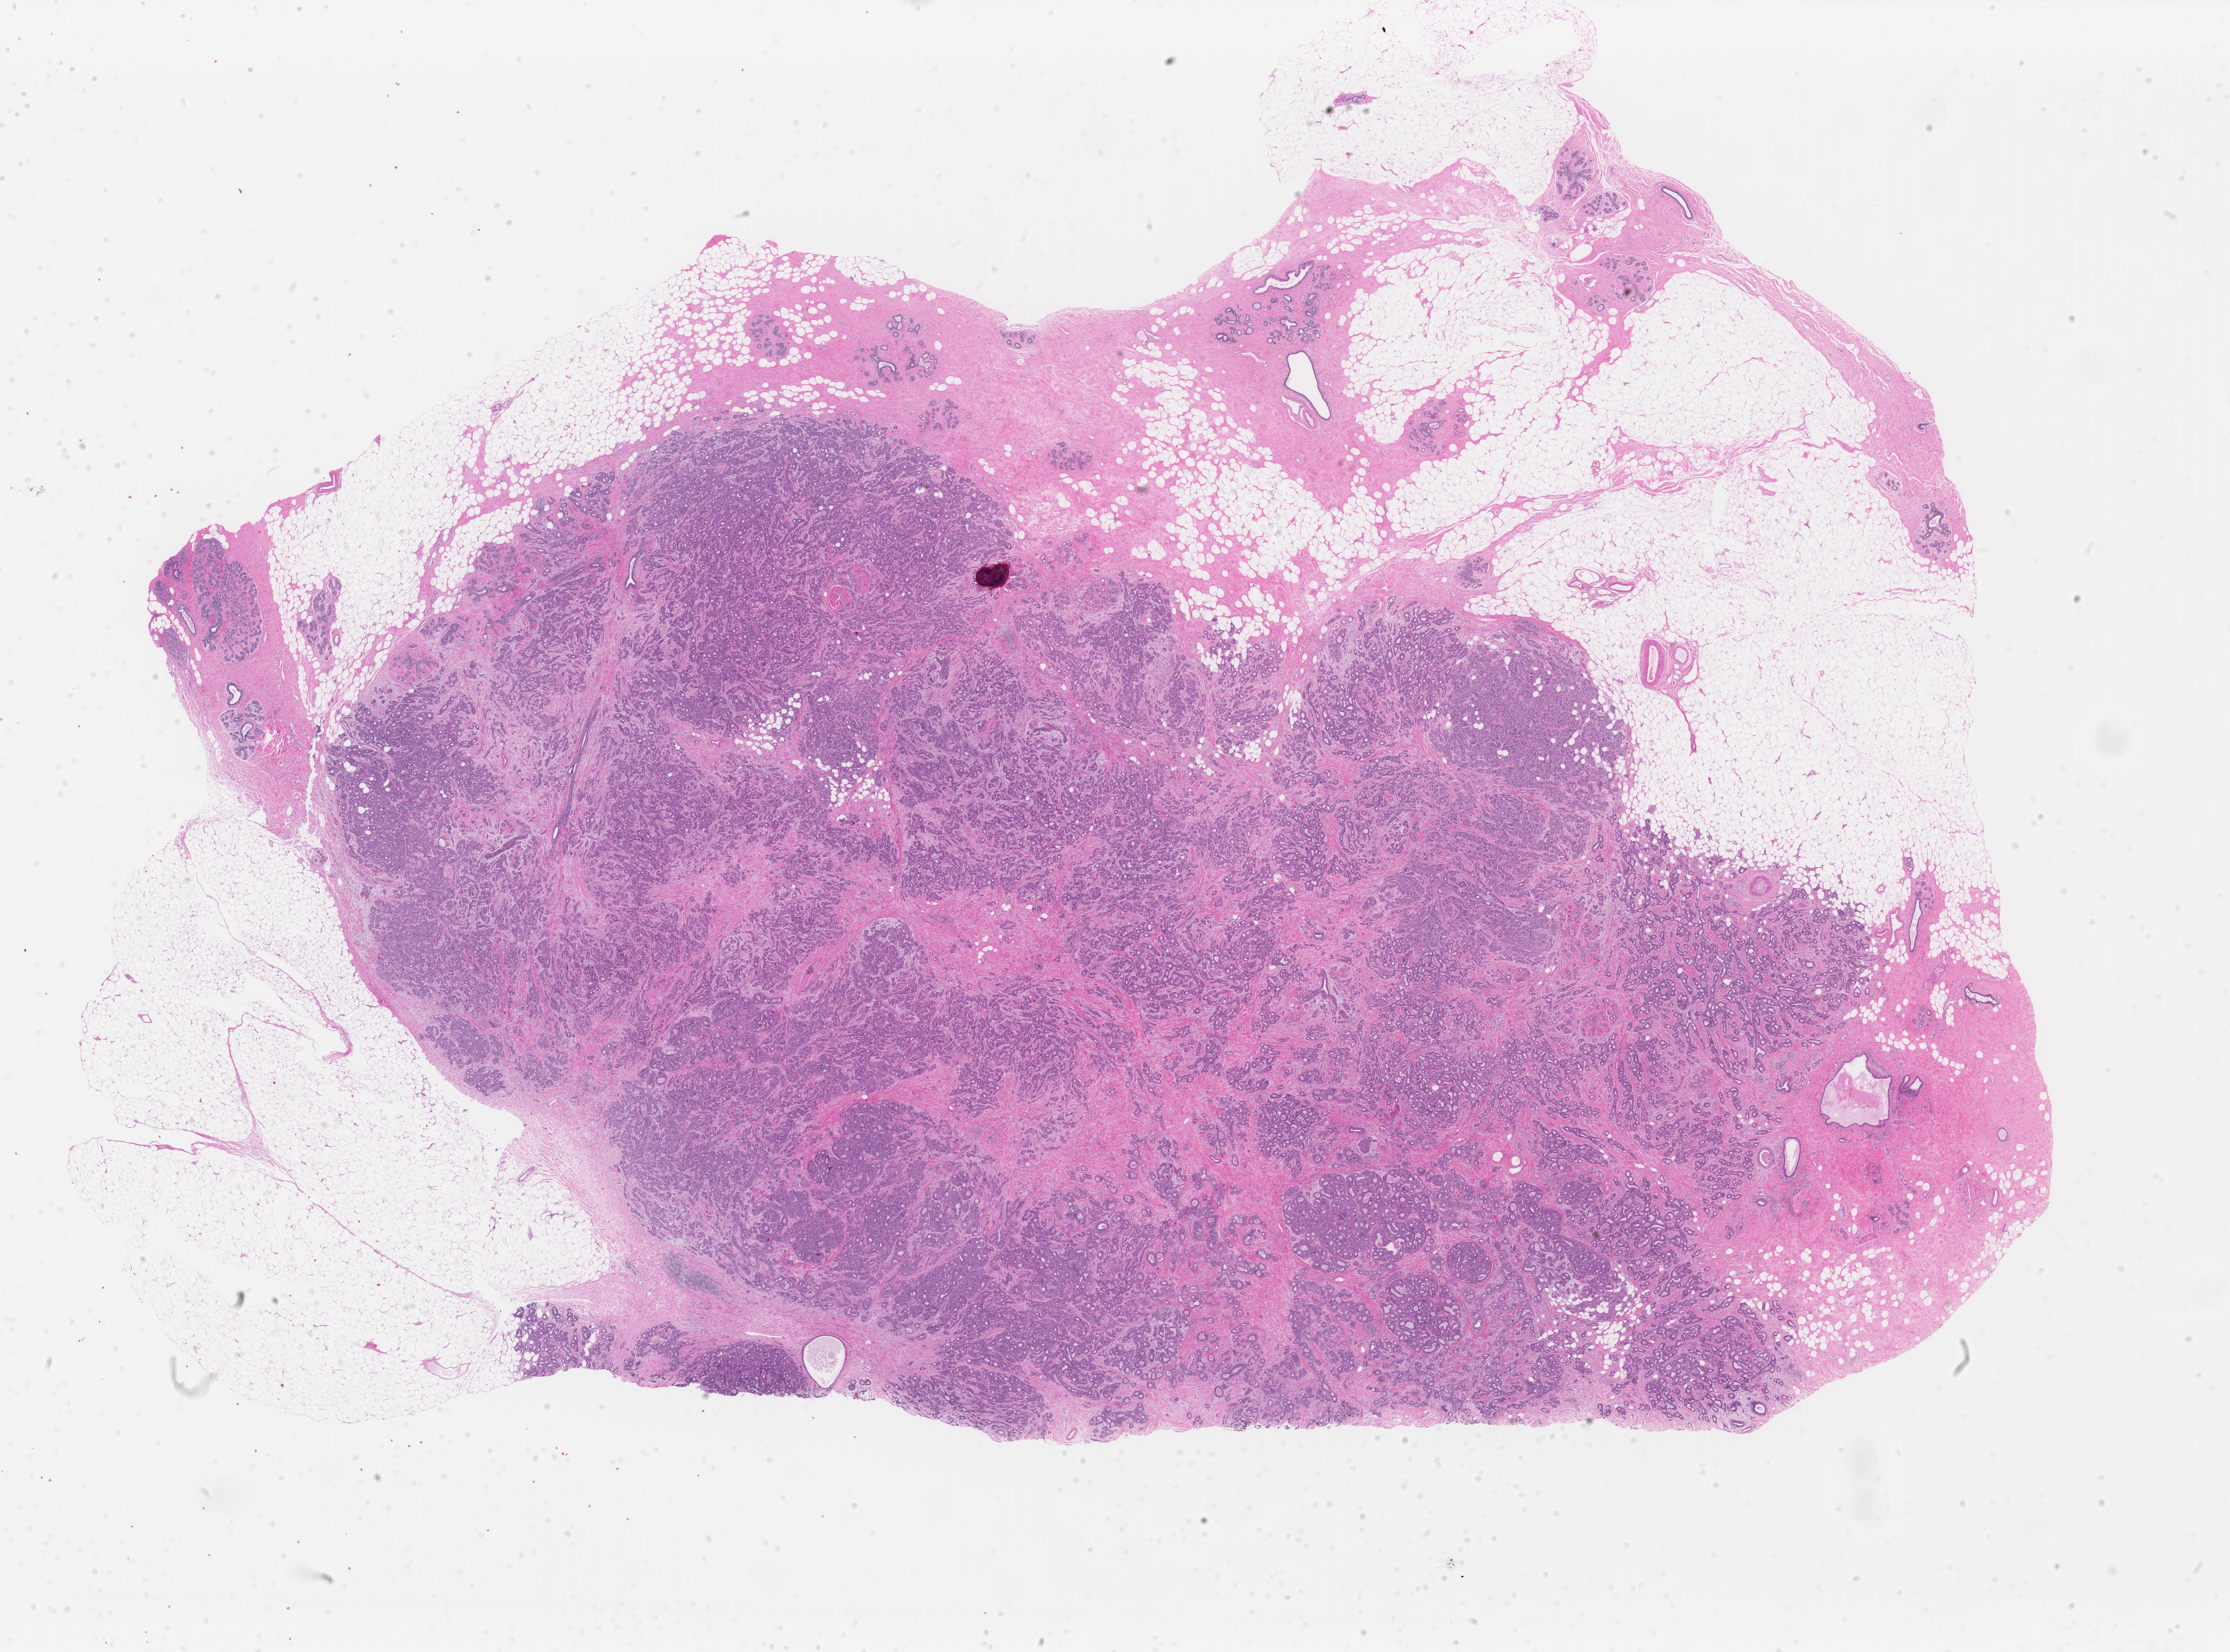
Hematoxylin and eosin (H&E) stained whole-slide image, shown as a low-resolution overview of the whole scanned area (about 30.2 x 22.4 mm, slide scanned at 40x). FFPE section. Primary tumour sample from the breast. Female, age 39 years at initial diagnosis.
* AJCC pathologic stage: IIA
* laterality: left
* pathologic diagnosis: Infiltrating duct carcinoma, NOS
* lymph nodes positive (case pathology): 0 of 4 examined